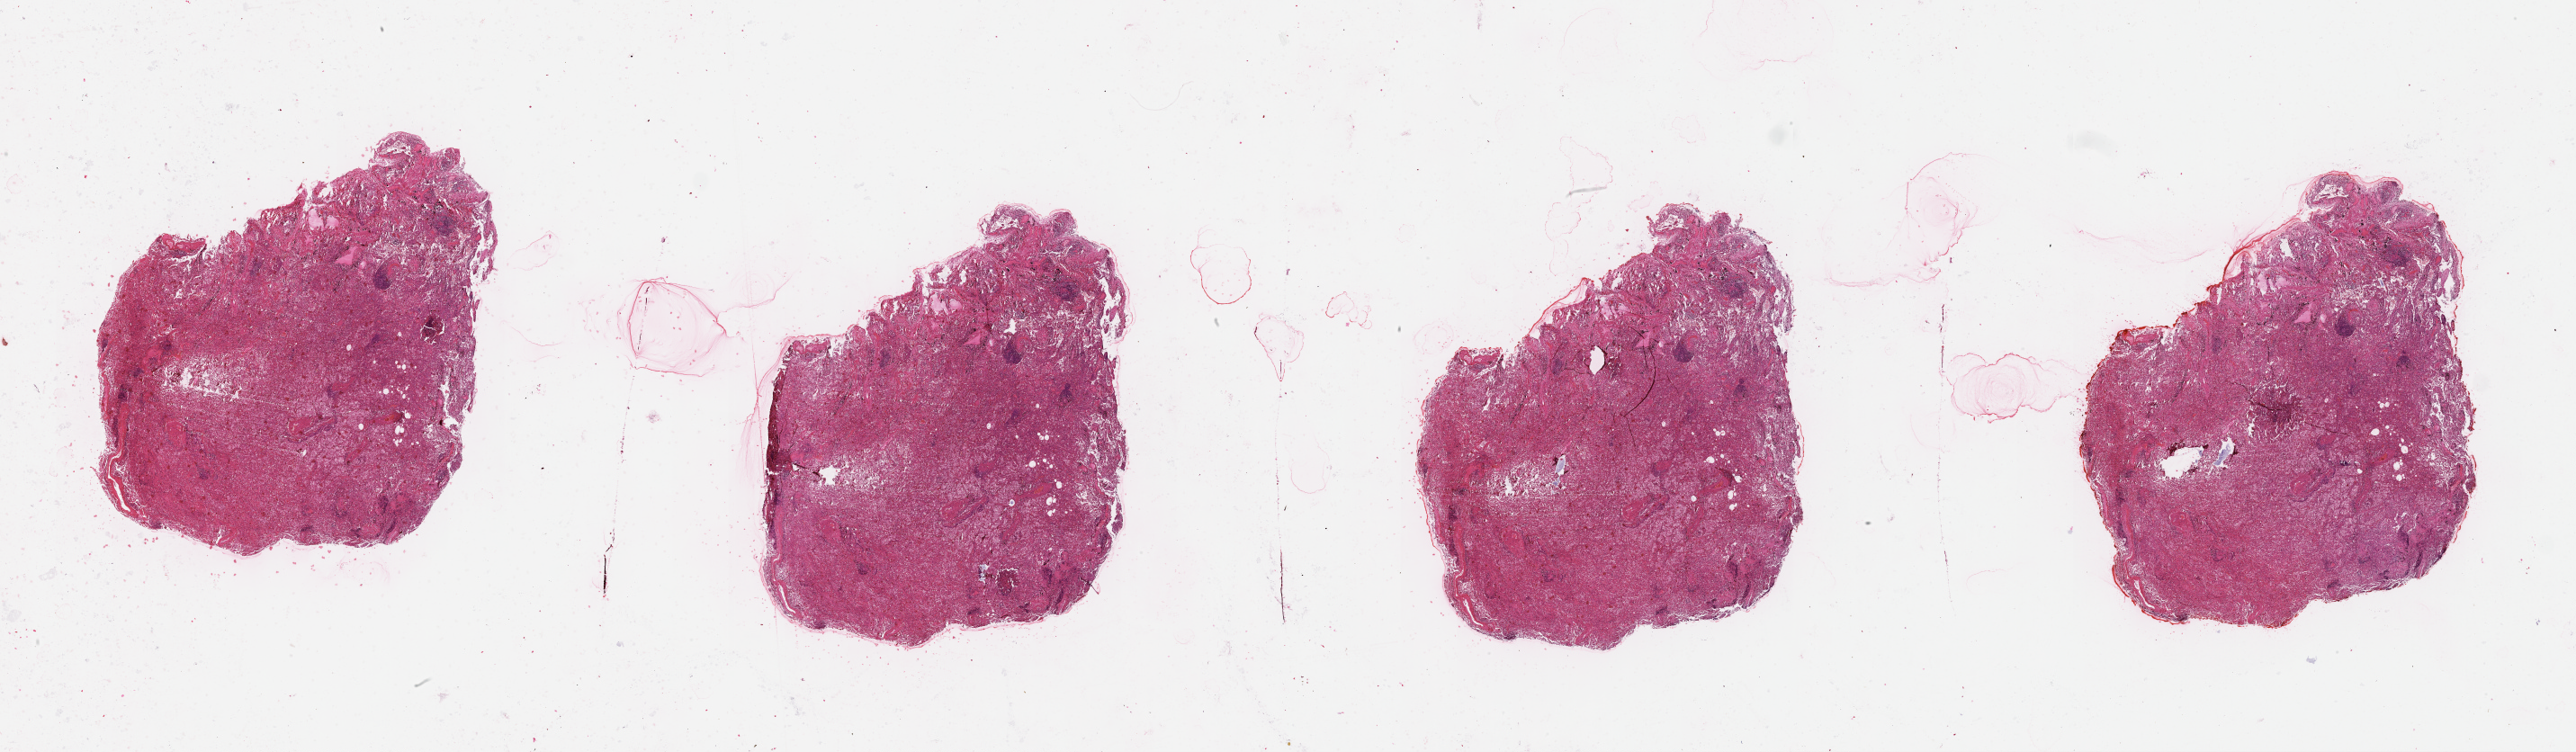
Whole-slide histology image, Hematoxylin and eosin (H&E) stained, a low-resolution overview of the entire scanned area, about 46.1 x 13.5 mm, lung, tissue type not recorded.
Patient diagnosis (cohort enrolment): squamous cell carcinoma (lung).